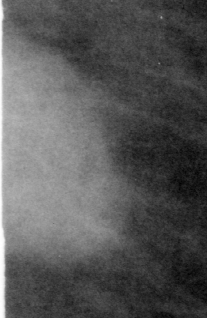
Crop from a digitized film mammogram around one marked abnormality; left breast; MLO view; BI-RADS breast density category 2 (scale 1–4).
Marked abnormality: mass, shape oval, margins circumscribed; BI-RADS assessment category 5; subtlety rating 5 on a 1 (subtle) to 5 (obvious) scale; pathology result (as recorded, not read from the image): malignant.